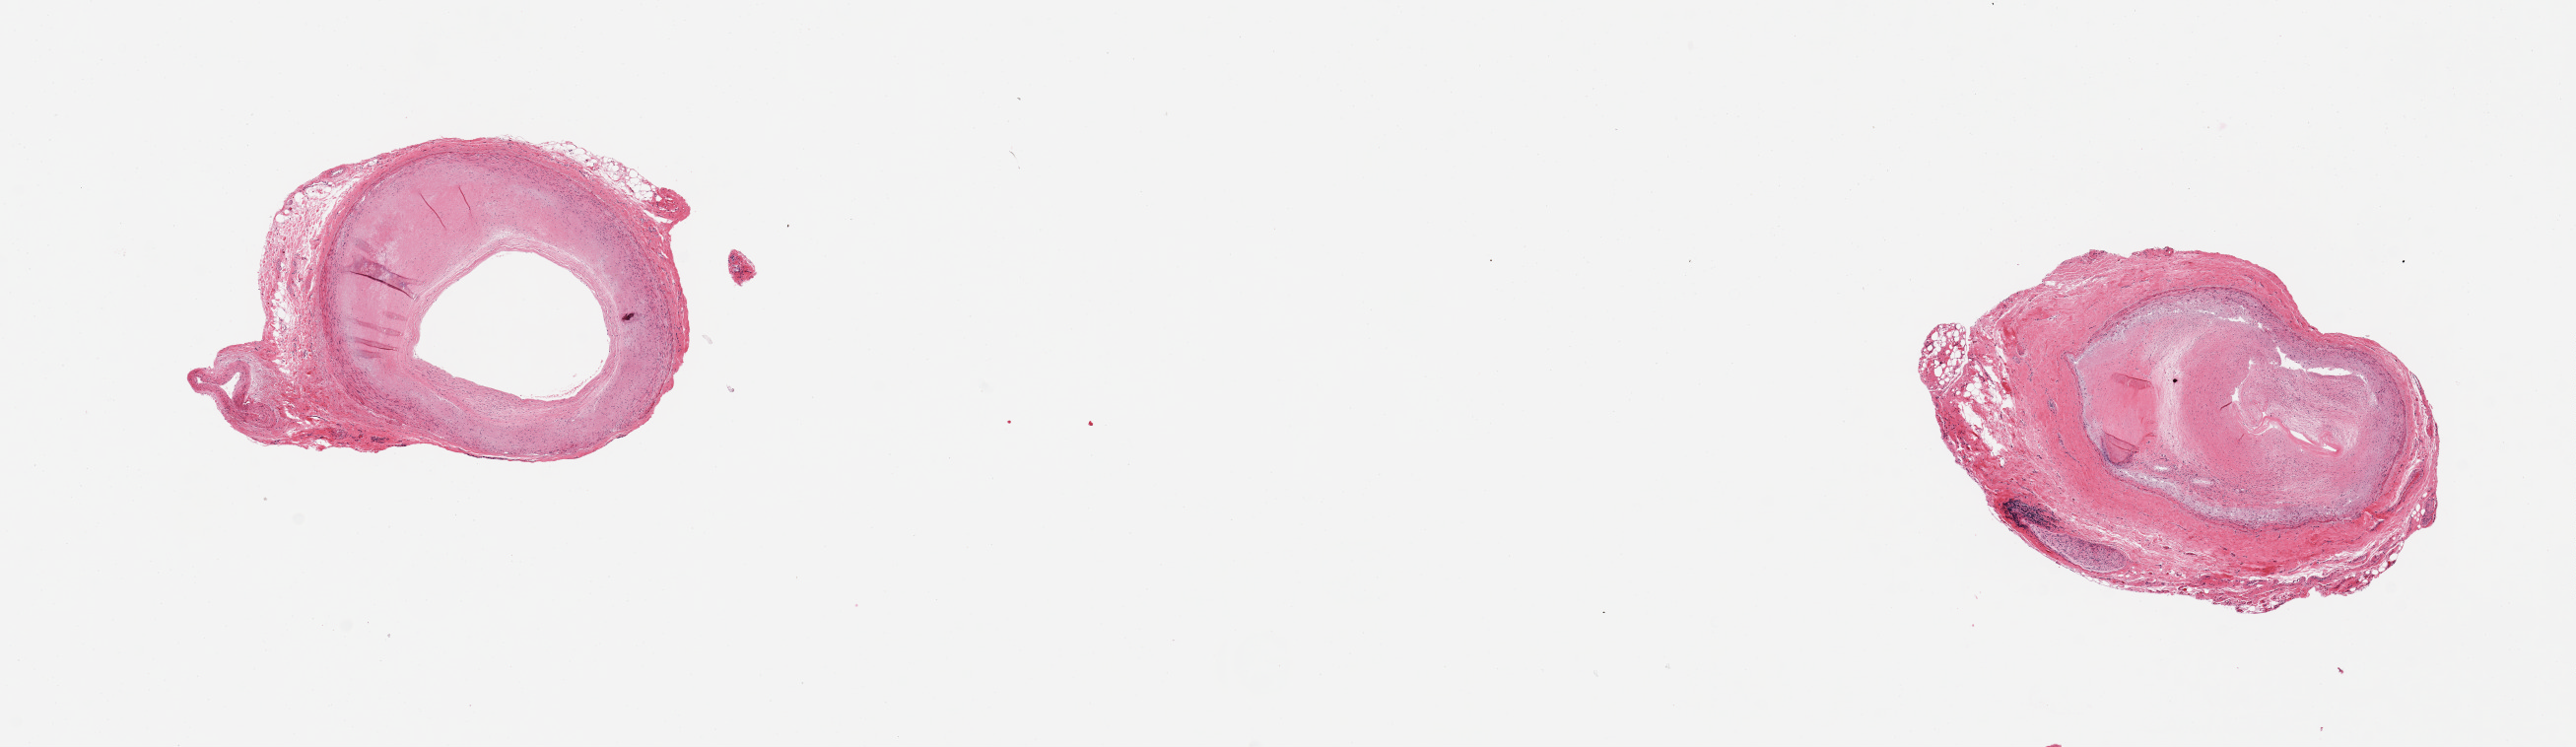
Whole-slide image, H&E stain — whole scanned area (about 20.7 x 6.0 mm) shown as a low-resolution overview. PAXgene-fixed paraffin-embedded (PFPE) section. Section of coronary artery (target tissue). Tissue donor sample. Donor: male.
Reviewer comment on this tissue sample: 2 pieces, subtotally occlusive atherosis.